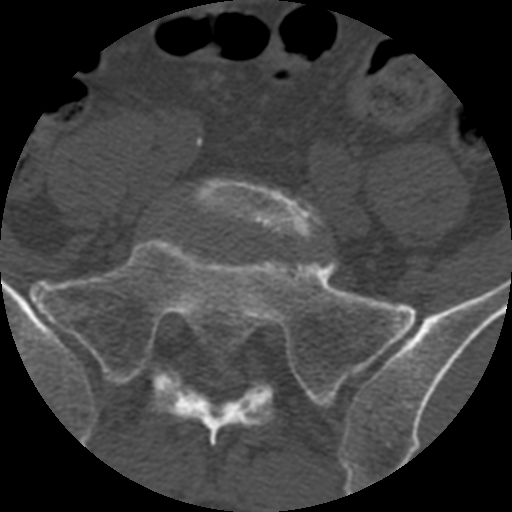
CT including the spine, one axial slice; slice 236 of 399 in the series (ordered by position); reconstruction kernel STANDARD; 120 kVp; bone window (W 1800 / L 400 HU); 1.25 mm slice thickness; 512 × 512 image matrix, field of view 160 × 160 mm. Patient age 71 years. Case-level facts recorded for this patient, not image findings: primary cancer: prostate.
Outlined on this slice (semi-automatic segmentation, software-assisted and operator-edited):
- L5 vertebra: box from (x=187, y=179) to (x=325, y=242) px